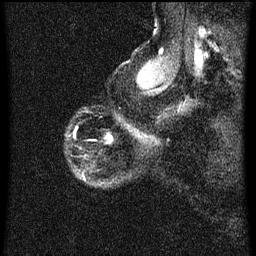
Breast MRI (dynamic contrast-enhanced), one sagittal slice; position 55 of 60 along the scan axis; dynamic contrast-enhanced series, image 2 of 3 at this slice position (ordered by acquisition); 1.5 T; TE 4.2 ms, TR 8 ms; 256 × 256 image matrix. Female patient, age 56 years.
Structures marked on this image (semi-automatic segmentation, software-assisted and operator-edited):
- analysis volume of interest (the breast-tissue region the enhancement analysis was run in; not a lesion): bounding box <110,136,113,141> (left, top, right, bottom; pixels)
- tumour enhancement mask (voxels above the 70 % enhancement threshold inside the analysis volume of interest): <110,136,113,141>